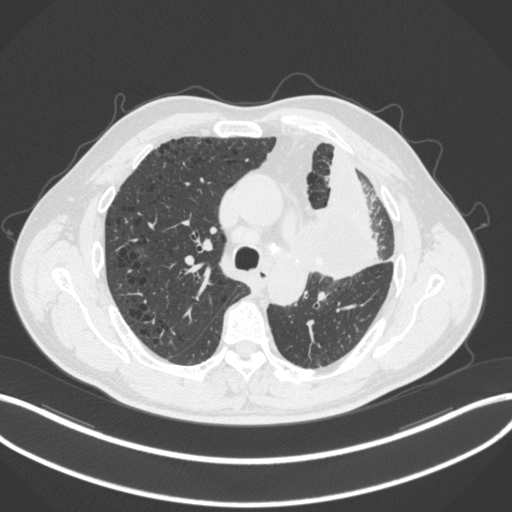
Chest CT, one axial slice; position 196 of 286 along the scan axis; reconstruction kernel B31f; 120 kVp; lung window (W 1500 / L -600 HU); 1 mm slice thickness; 512 × 512 image matrix, field of view 400 × 400 mm. Patient: male, 68 years. Case-level facts recorded for this patient, not image findings: clinical TNM (as recorded): T3 N3 M1.
Structures marked on this image (bounding box drawn by a radiologist):
- lung tumour (recorded histology: adenocarcinoma): box from (x=299, y=193) to (x=383, y=287) px